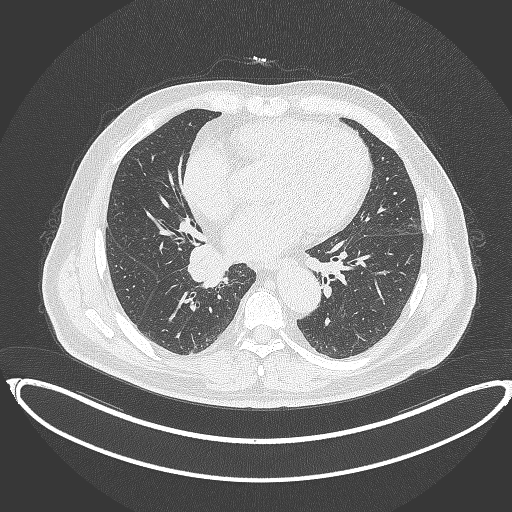
Chest CT, one axial slice; slice 184 of 387 in the series (ordered by position); lung window (W 1500 / L -600 HU); 1 mm slice thickness; 512 × 512 image matrix, field of view 448 × 448 mm. Male patient, age 61 years. Case-level facts recorded for this patient, not image findings: clinical TNM (as recorded): T1b N1 M0.
Outlined on this slice (rectangle marked by the reading radiologist):
- lung tumour (recorded histology: squamous cell carcinoma): bounding box [x1, y1, x2, y2] px = [185, 243, 230, 290]